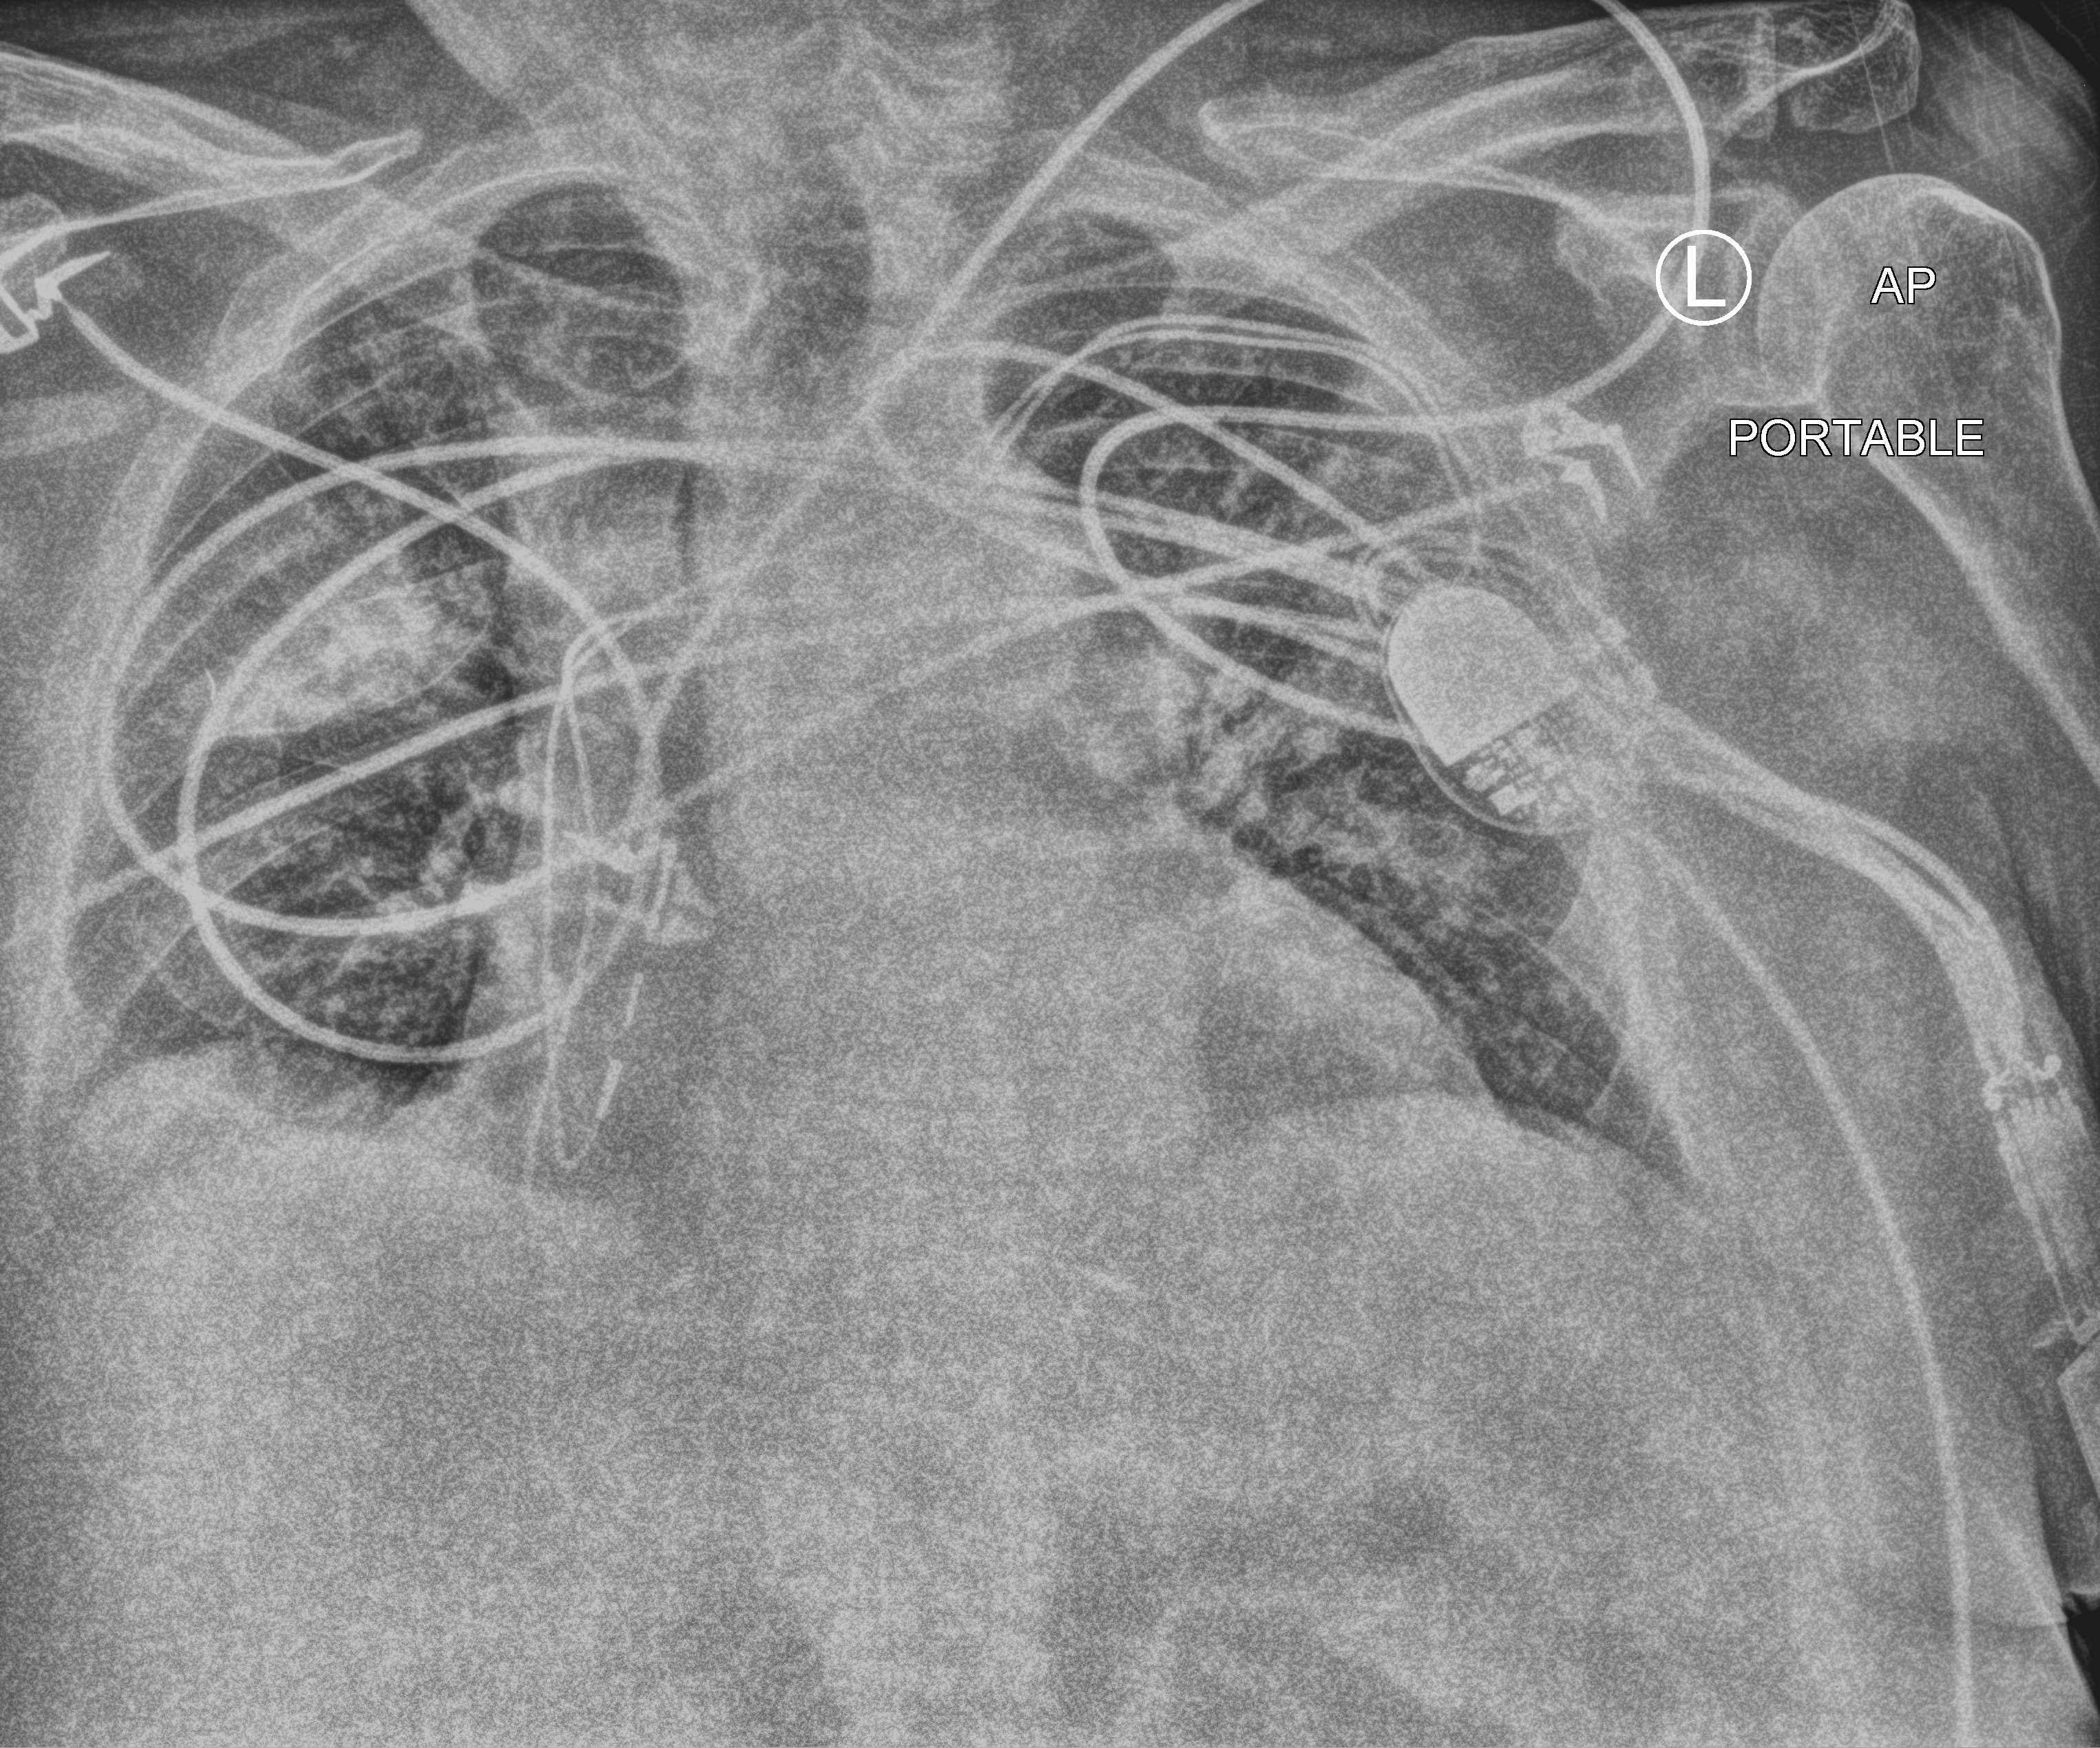
Bedside chest radiograph (computed radiography). Male patient hospitalised with COVID-19, age 75–90 years.
Admission-level facts for this patient (not findings on this image; timing relative to this image not recorded): mechanically ventilated during this hospital stay: no; admitted to intensive care during this hospital stay: no; chronic kidney disease (admission record): no.